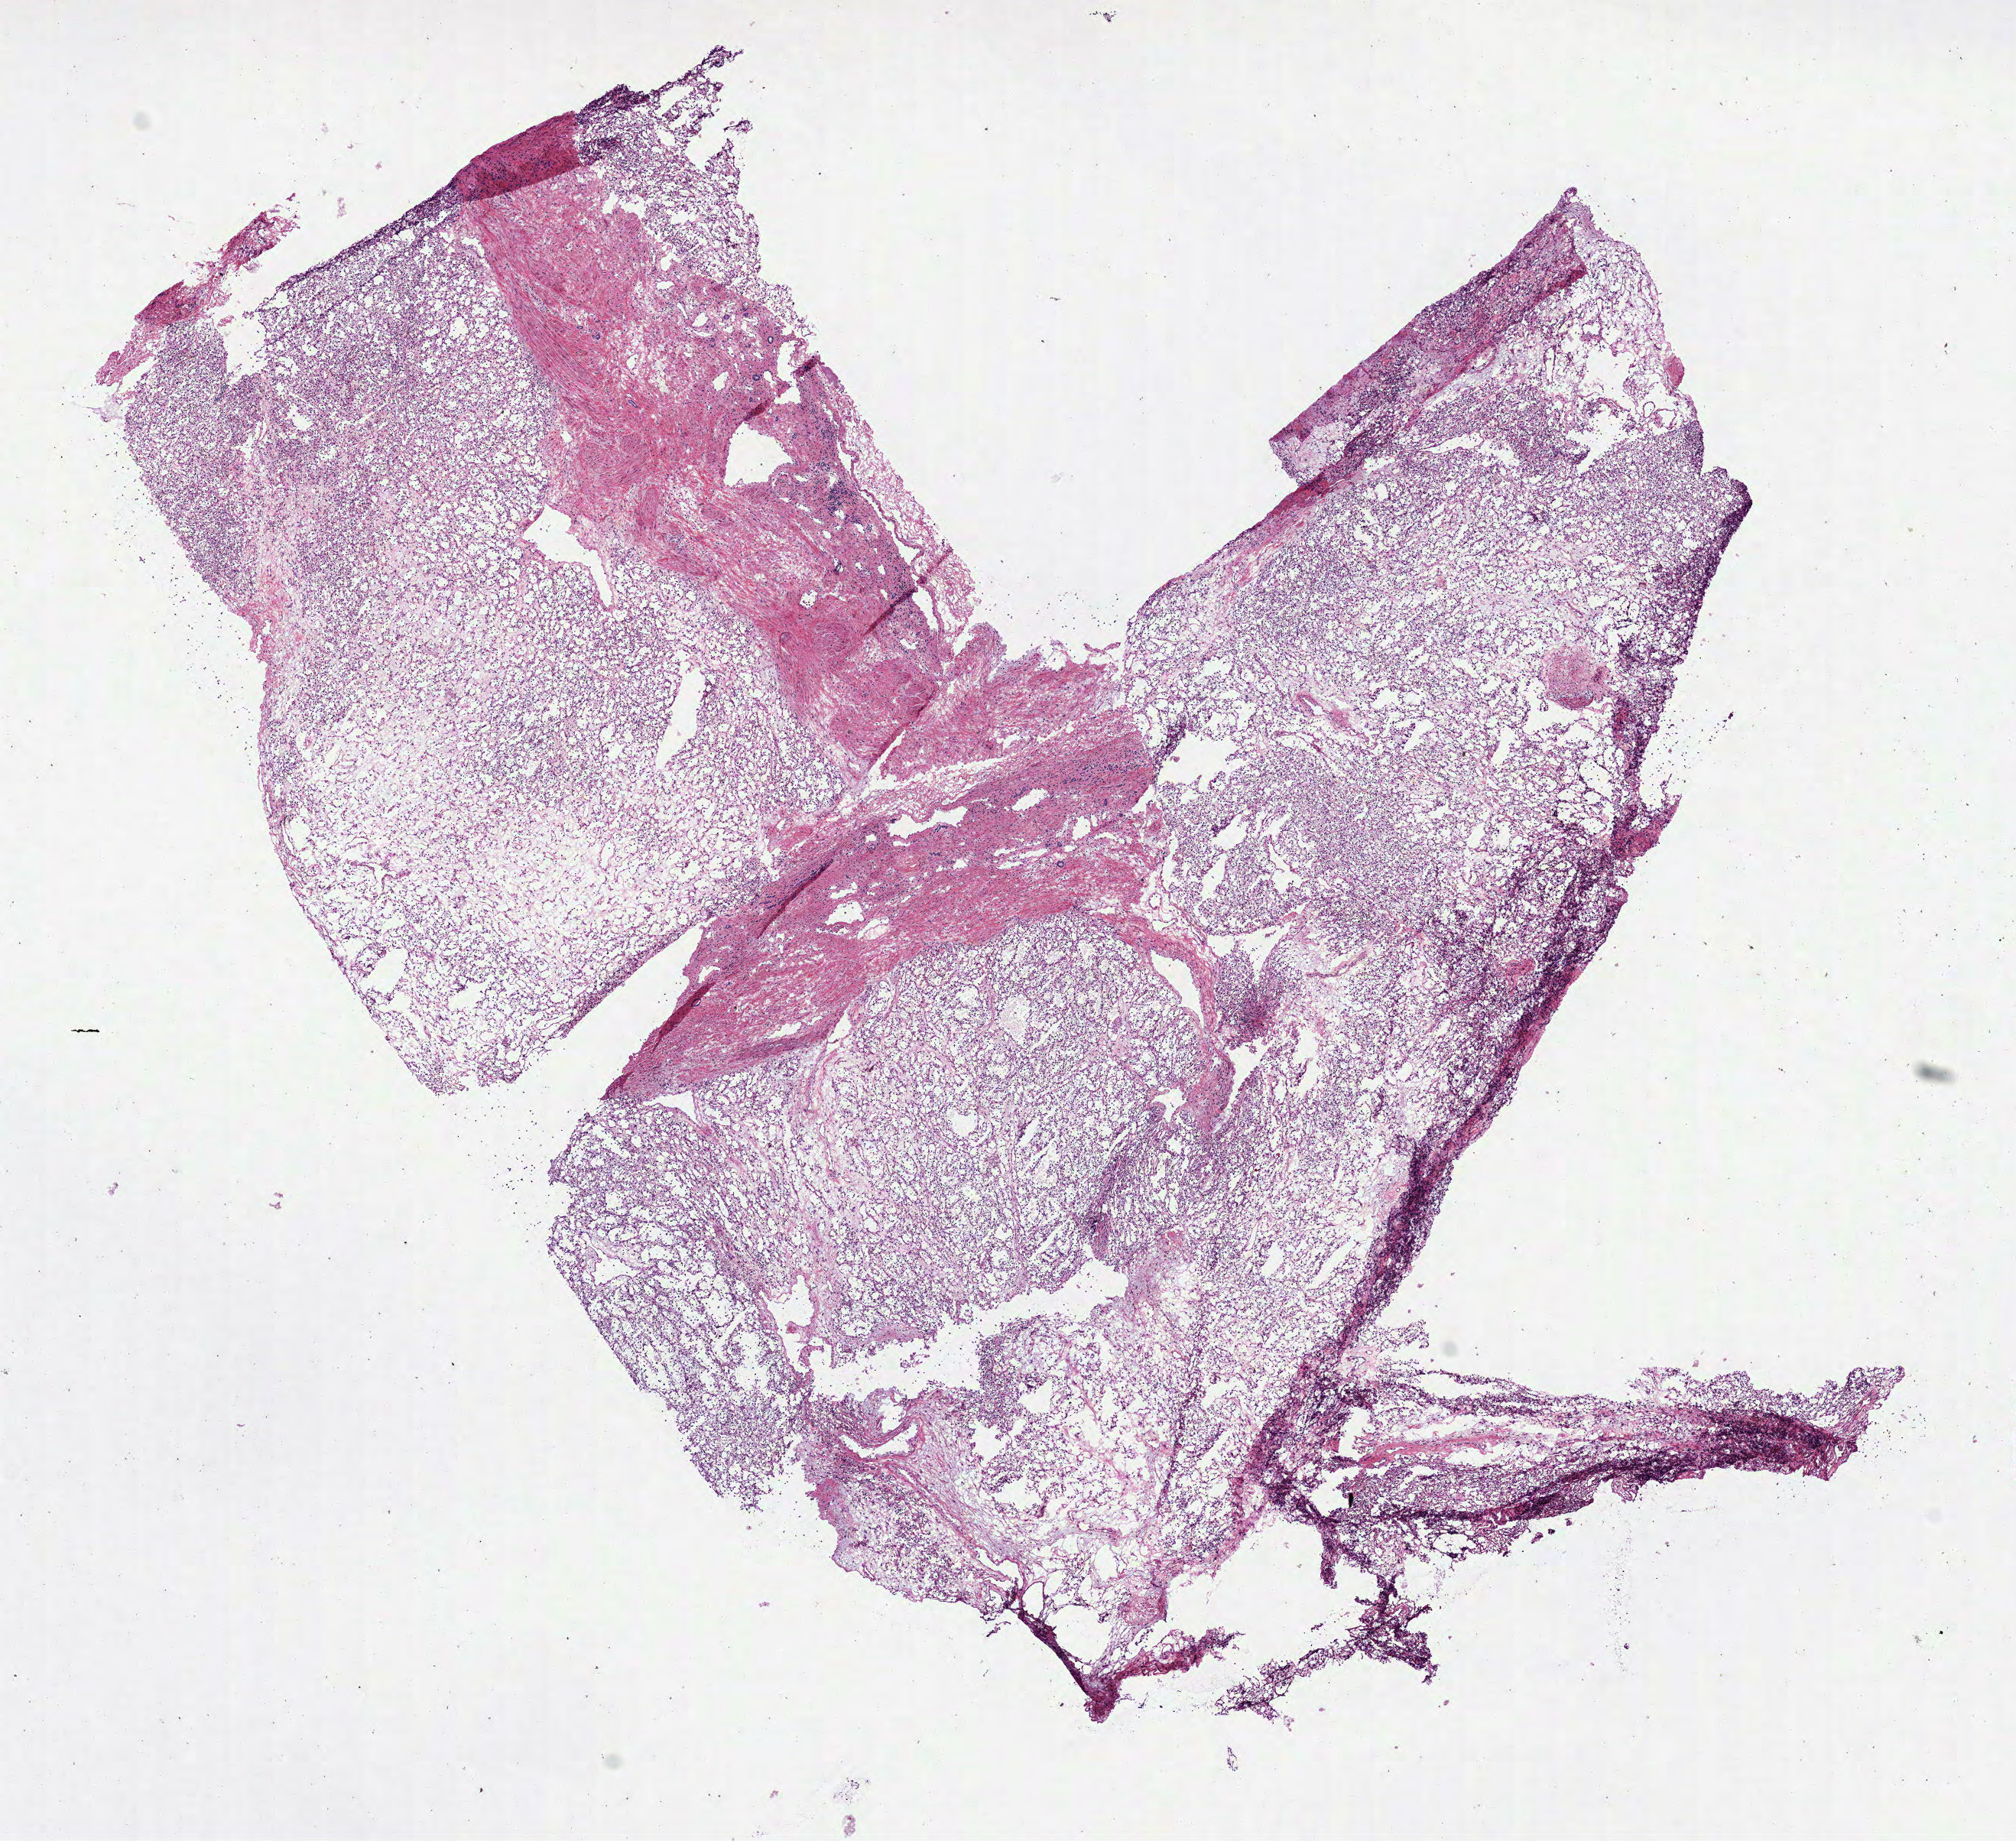
H&E whole-slide image, shown as a low-resolution overview of the whole scanned area (about 10.6 x 9.7 mm, acquisition: 40x scan); frozen section; sample: primary tumour, kidney. Female, age 47 years at initial diagnosis. Histologic grade: G1 (well differentiated). Composition of this section per pathologist review: tumour cells 85%, tumour nuclei 85%, normal cells 0%, stromal cells 15%, necrosis 0%.
Pathologic diagnosis: Clear cell adenocarcinoma, NOS. AJCC pathologic stage: I (6th edition).